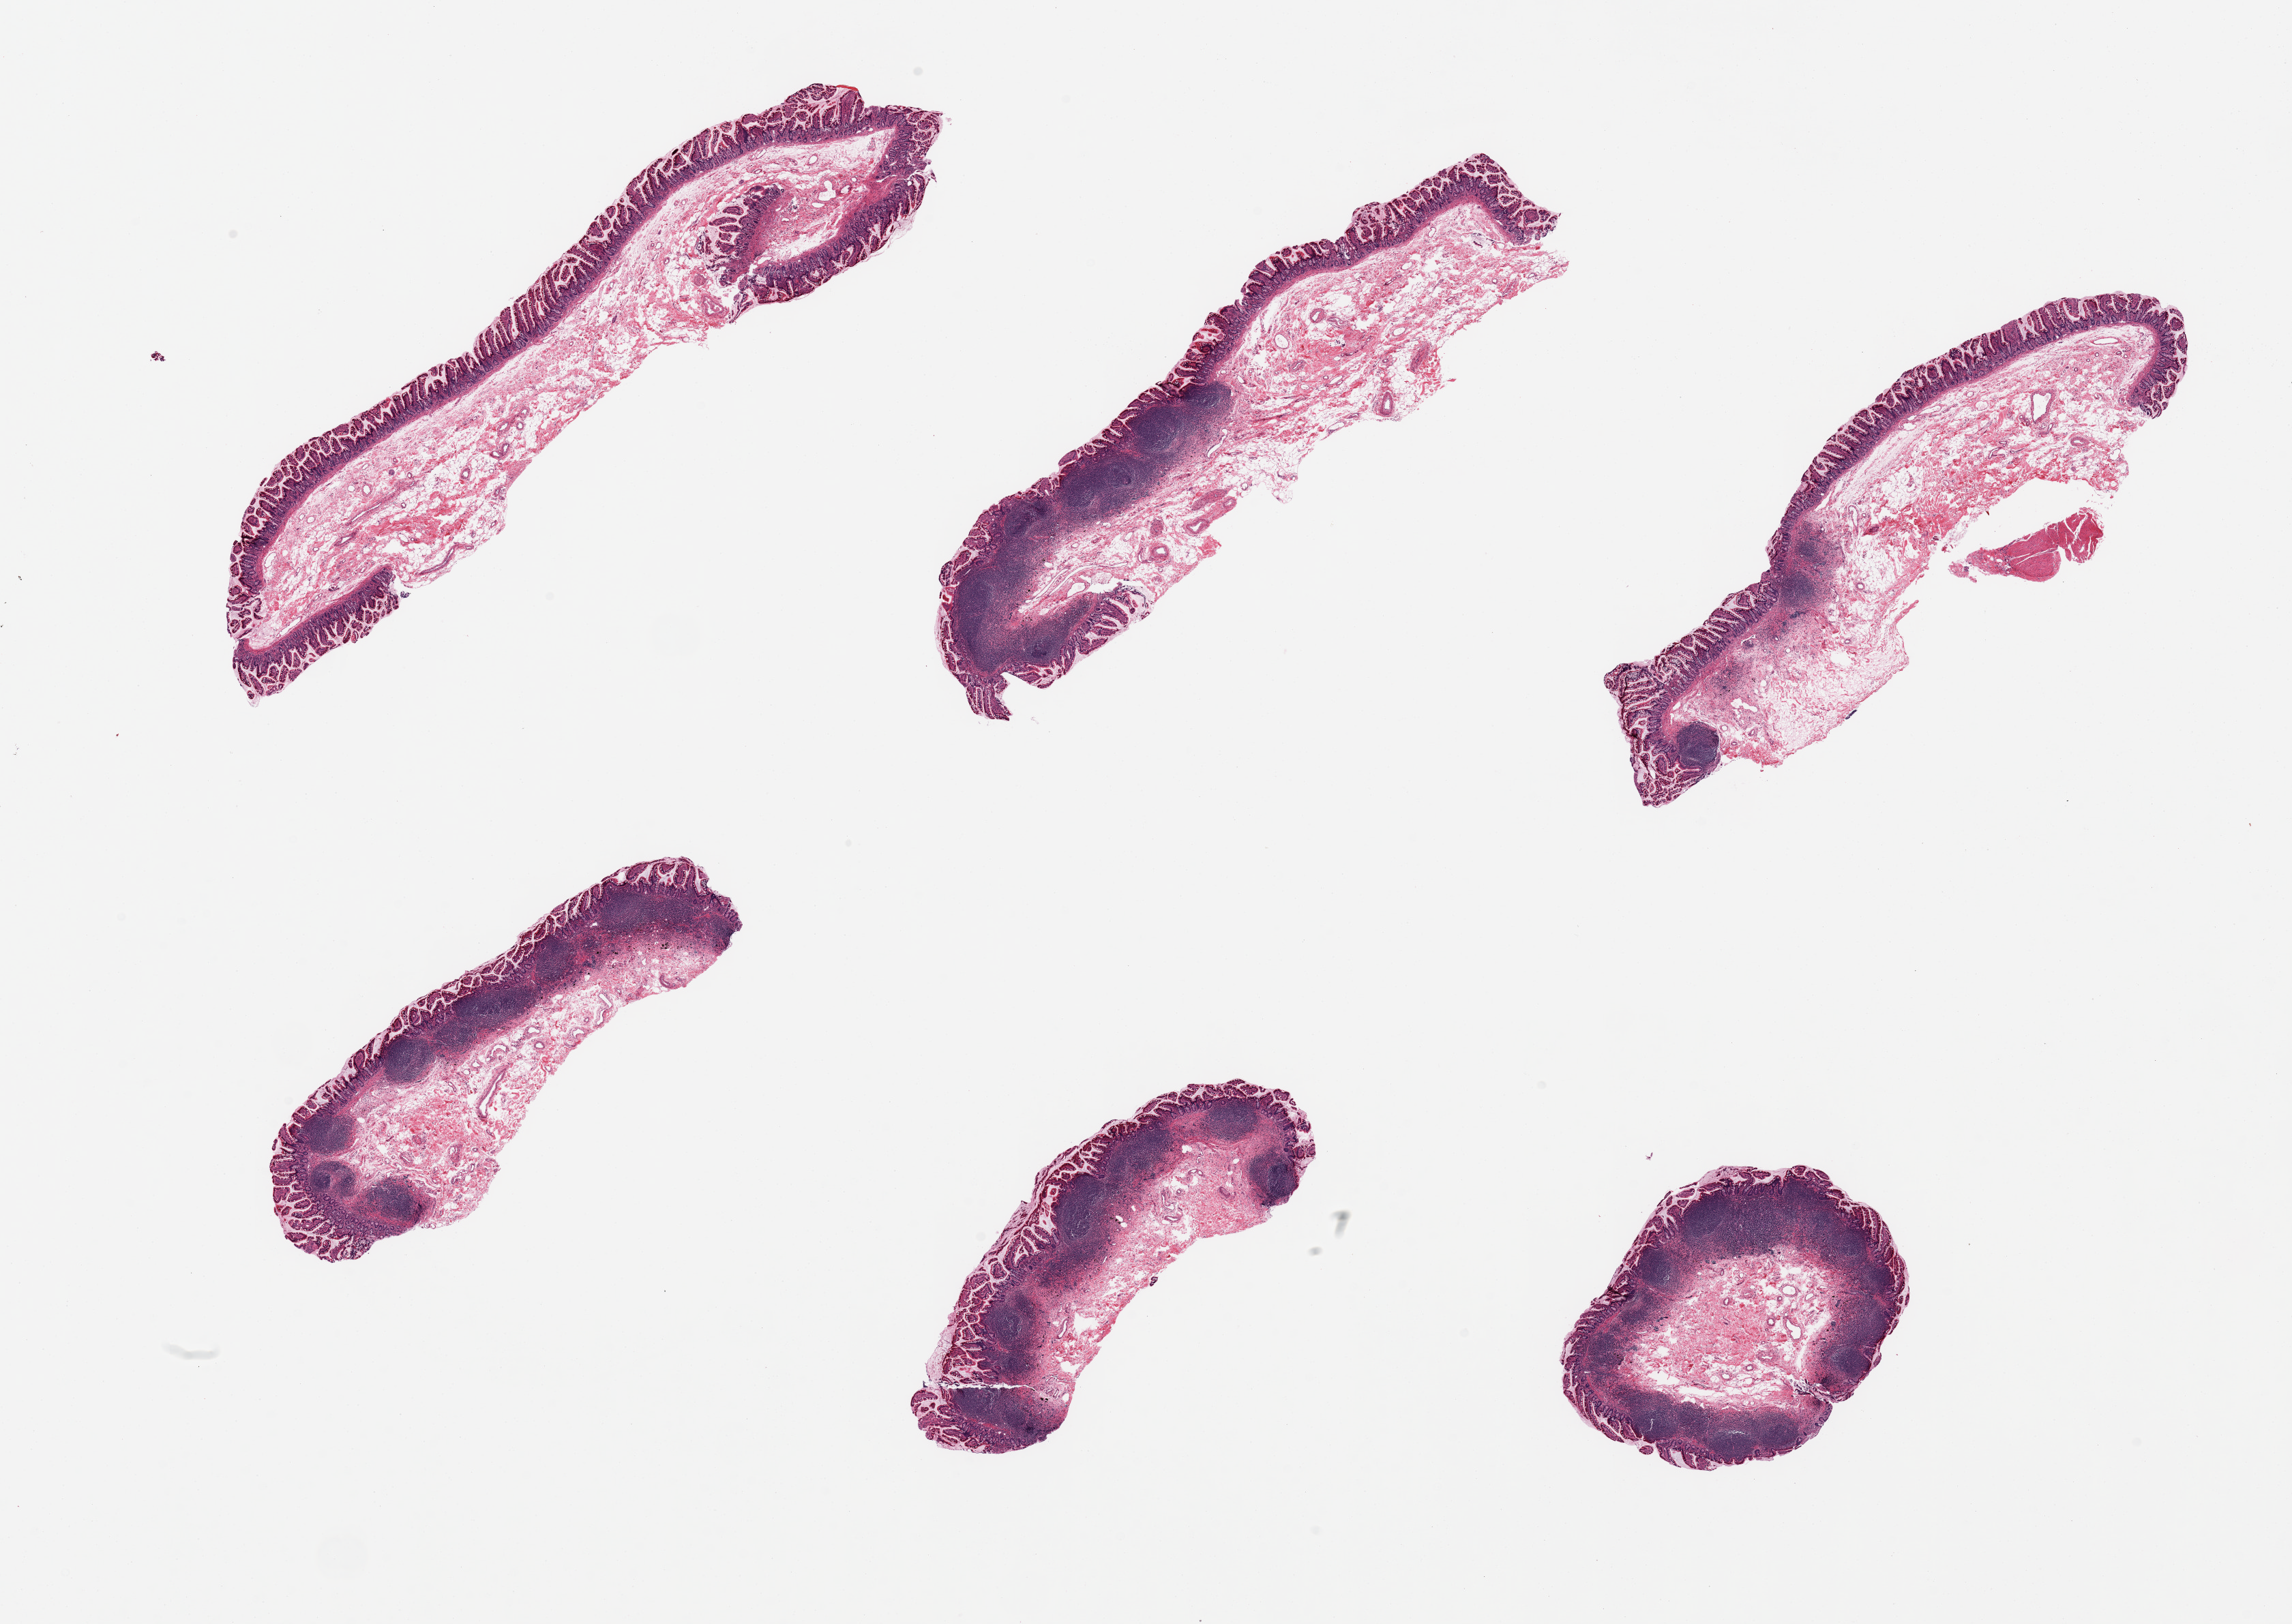
Digitized H&E-stained section, brightfield, low-resolution overview of the scanned area, about 26.6 x 18.8 mm; PAXgene-fixed paraffin-embedded (PFPE) section; sampled site (target tissue): ileum; tissue donor sample.
Pathologist's review note for this sample: 6 pieces, abundant lymphoid aggregates.